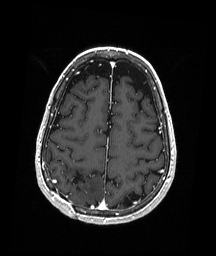
Brain MRI from a brain-tumour surgery series, one axial slice. Position 64 of 192 along the scan axis. T1-weighted post-contrast. 216 × 256 image matrix, field of view 211 × 250 mm. Case-level facts recorded for this patient, not image findings: histopathology: Astrocytoma; WHO grade: 3; IDH mutation: yes.
Annotated regions visible in this slice (expert manual segmentation):
- previous resection cavity: bounding box (x1, y1, x2, y2) in pixels: (68, 171, 84, 191)